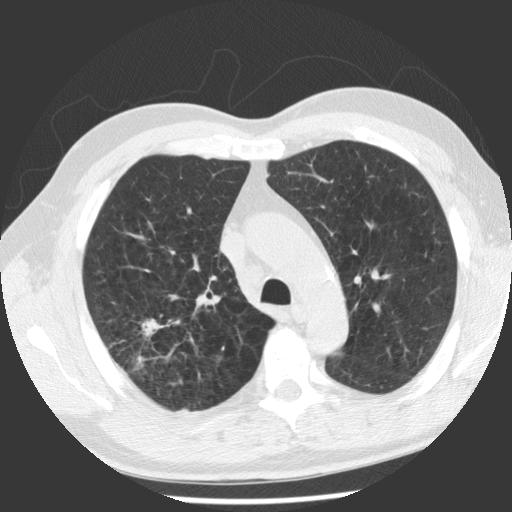
Chest CT (low-dose screening protocol), one axial image. First (baseline) screen. Lung window (W 1500 / L -600 HU). 2.5 mm slice thickness. Standard (soft-tissue) reconstruction kernel (STANDARD). Male participant, aged 62 years at enrolment. Former smoker at enrolment.
Expert-annotated lung lesion, bounding box [x1, y1, x2, y2] px = [111, 300, 187, 374]. The screening reader recorded 2 non-calcified nodules or masses ≥4 mm on this exam (right upper lobe, right upper lobe); which of them this box marks is not recorded. Official screen result: positive, change unspecified: nodule(s) >= 4 mm or enlarging nodule(s), mass(es), or other non-specific abnormalities suspicious for lung cancer. Participant outcome: lung cancer diagnosed 71 days after this screen — adenocarcinoma, NOS, right upper lobe, poorly differentiated (G3), stage IV (AJCC 6th edition), 30 mm at pathology.